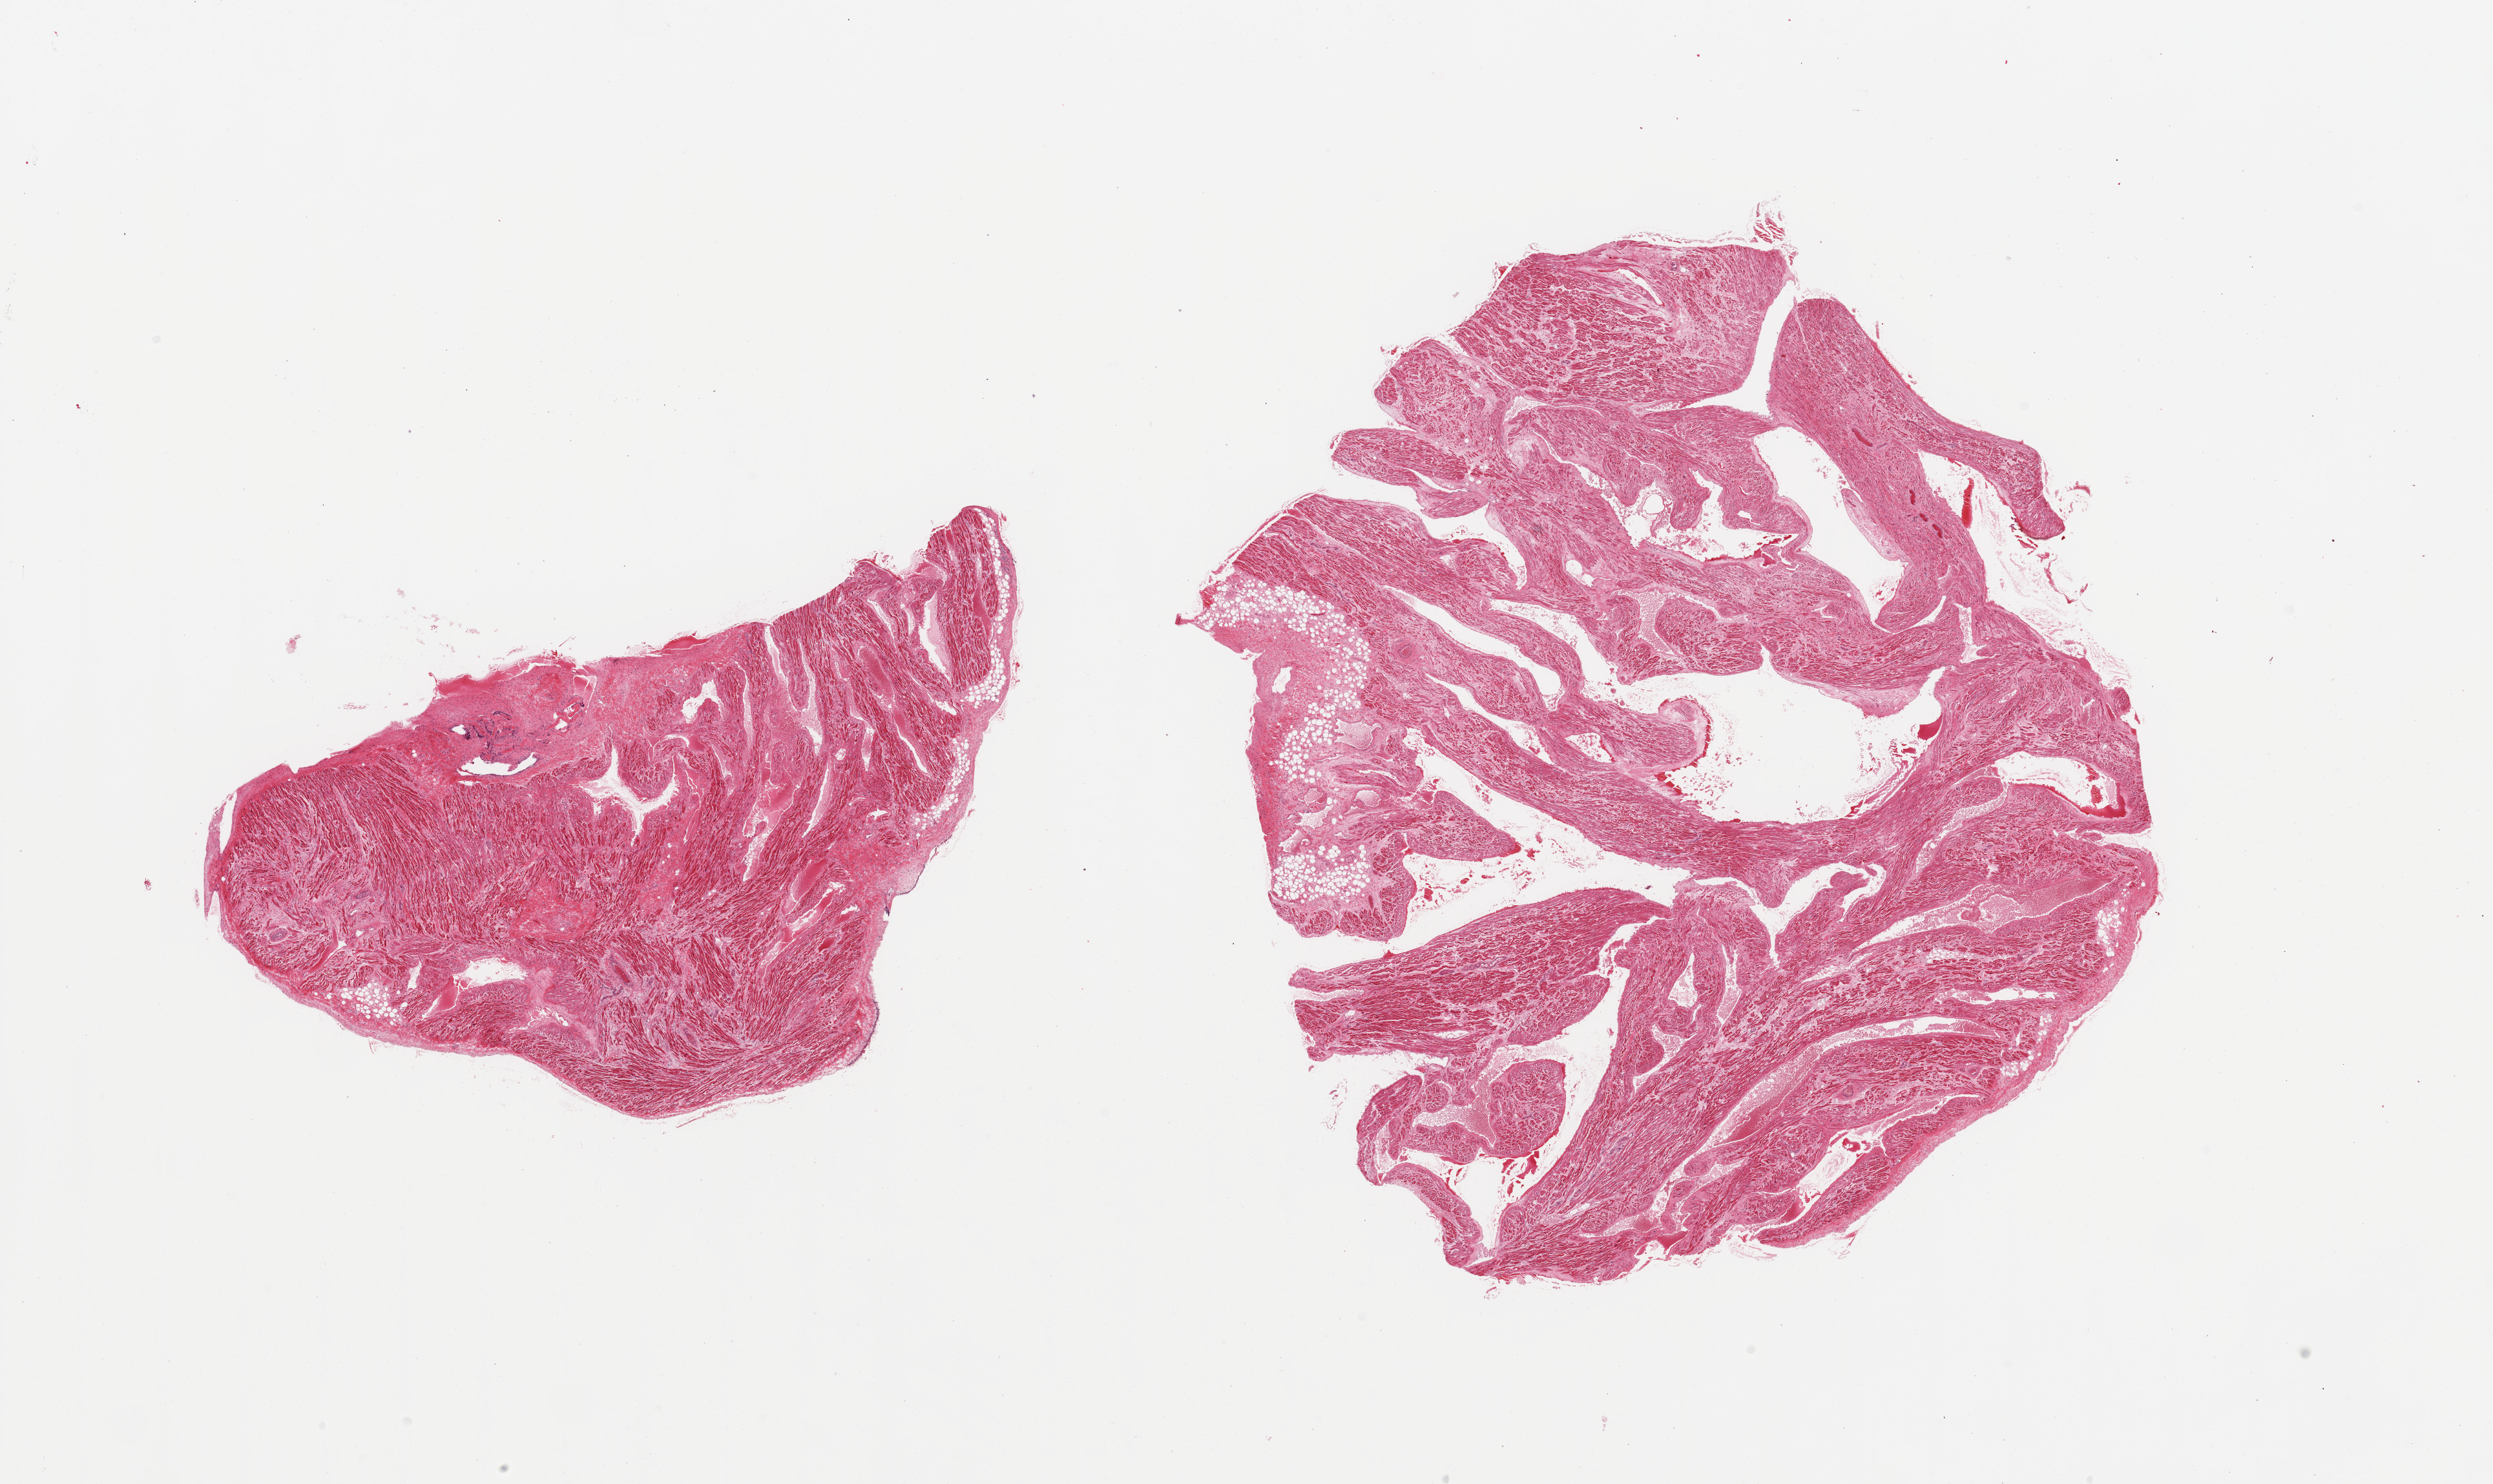
Haematoxylin and eosin whole-slide image — low-resolution overview of the scanned area, about 30.5 x 18.2 mm (acquisition: 20x scan), PAXgene-fixed paraffin-embedded (PFPE) section, sampled site (target tissue): auricular appendage, tissue donor sample. Donor: male.
Review note (as recorded): 2 pieces, no abnormalities.